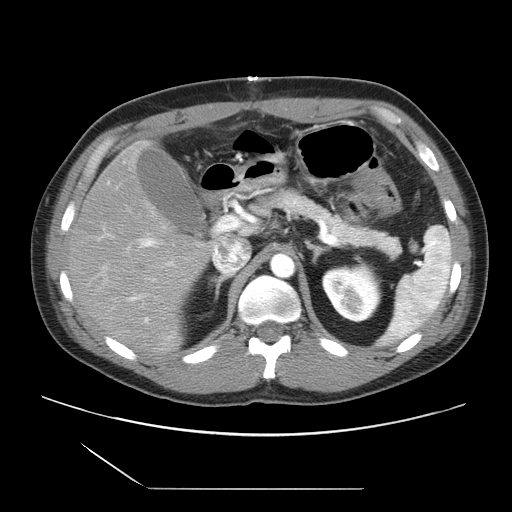
Contrast-enhanced abdominal CT, one axial slice. Slice 15 of 39 in the series (ordered by position). 120 kVp. Intravenous contrast given. Soft-tissue window (W 400 / L 40 HU). 512 × 512 image matrix, field of view 395 × 395 mm. Male patient, age 39 years. Case-level facts recorded for this patient, not image findings: diagnosis: colorectal cancer liver metastases, imaged before liver resection; multiple liver metastases: yes; largest metastasis: 1.3 cm; disease in both lobes: no.
Structures marked on this image (expert manual segmentation):
- hepatic veins: bounding box [x1, y1, x2, y2] px = [214, 240, 248, 274]
- liver: [67, 145, 215, 355]
- planned liver remnant (the part of the liver to remain after resection): [127, 144, 143, 161]
- portal vein (with intrahepatic branches): [98, 182, 240, 324]